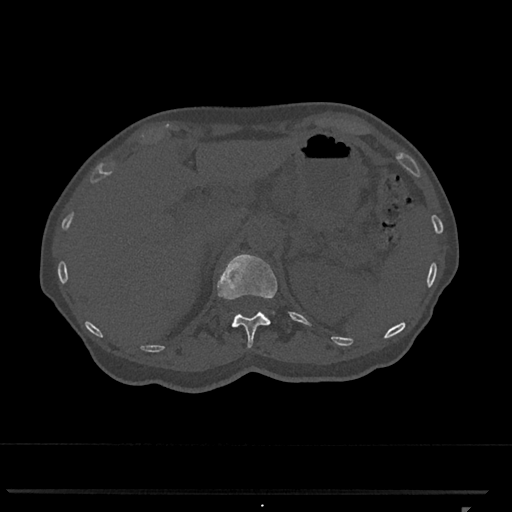
CT including the spine, one axial slice. Slice 450 of 793 in the series (ordered by position). Reconstruction kernel Br40s/3. 120 kVp. Bone window (W 1800 / L 400 HU). 0.5 mm slice thickness. 512 × 512 image matrix, field of view 380 × 380 mm. Patient: female, 62 years. From the clinical record (not read from this slice): primary cancer: renal.
Annotated regions visible in this slice (semi-automatic segmentation, software-assisted and operator-edited):
- T12 vertebra: box from (x=217, y=254) to (x=278, y=349) px